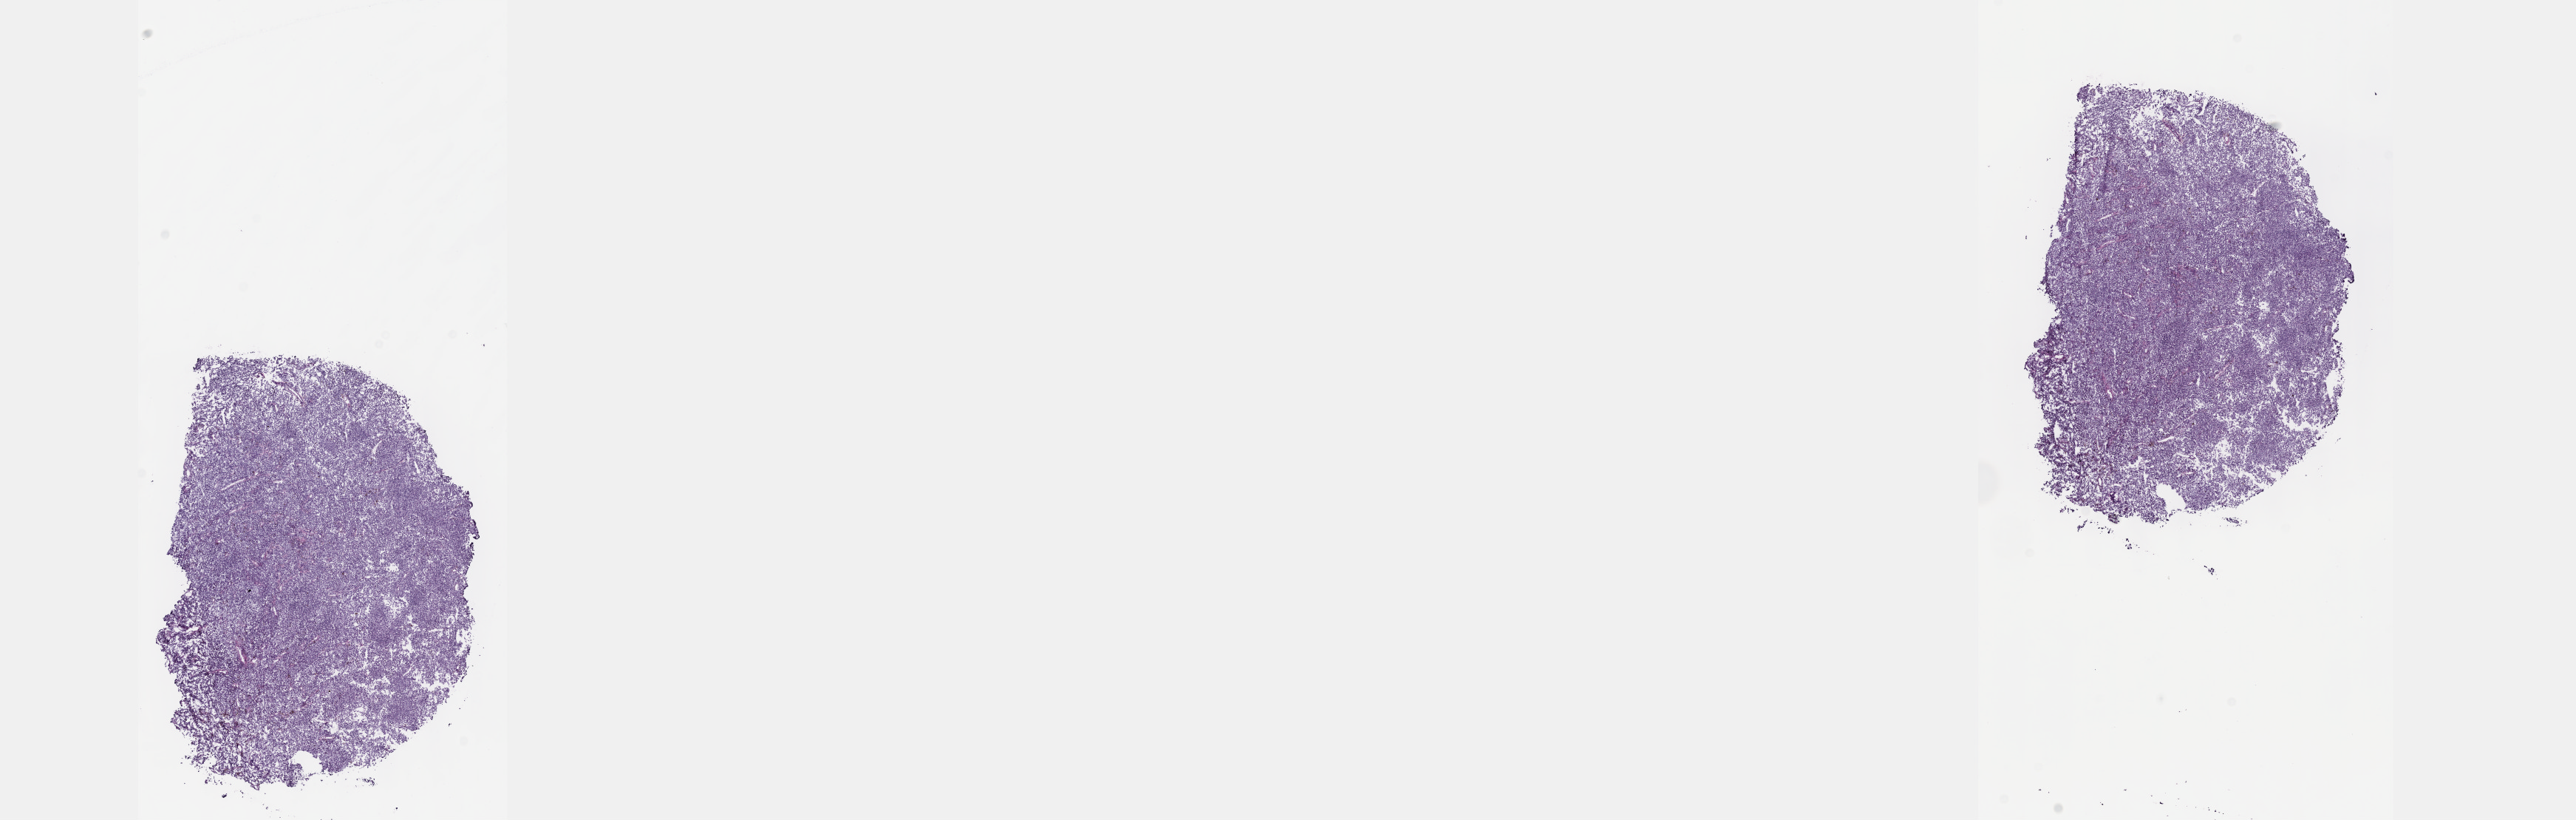
Whole-slide histology image, Hematoxylin and eosin (H&E) stained, low-resolution overview of the scanned area, about 28.2 x 9.0 mm (from a 40x scan). Frozen section from the top of the tissue portion. Uvea, primary tumour sample. Patient: male, age at initial diagnosis 53 years. Slide review estimates, as recorded: tumour cells 100%, tumour nuclei 80%, normal cells 0%, stromal cells 0%, necrosis 0%. Inflammatory infiltration, as recorded: lymphocyte infiltration 2%, monocyte infiltration 0%, neutrophil infiltration 0%.
AJCC pathologic stage: IIIA (7th edition). TNM: T4a N0 M0. Pathologic diagnosis: Epithelioid cell melanoma (choroid).